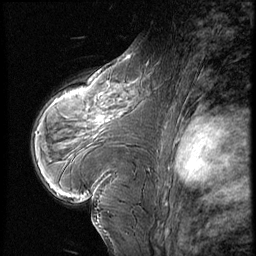
Breast MRI (dynamic contrast-enhanced), one sagittal slice; slice 39 of 60 in the series (ordered by position); 3 images stored at this slice position (order not interpretable as contrast timing); 1.5 T; TE 4.2 ms, TR 8.9 ms; 2.5 mm slice thickness; 256 × 256 image matrix. Patient: female, 39 years. Case-level facts recorded for this patient, not image findings: setting: breast cancer imaged before/during neoadjuvant chemotherapy; receptor status: HER2-positive.
Annotated regions visible in this slice (semi-automatically segmented with operator editing):
- analysis volume of interest (the breast-tissue region the enhancement analysis was run in; not a lesion): bounding box <72,79,141,135> (left, top, right, bottom; pixels)
- tumour enhancement mask (voxels above the 140 % enhancement threshold inside the analysis volume of interest): <96,117,106,122>